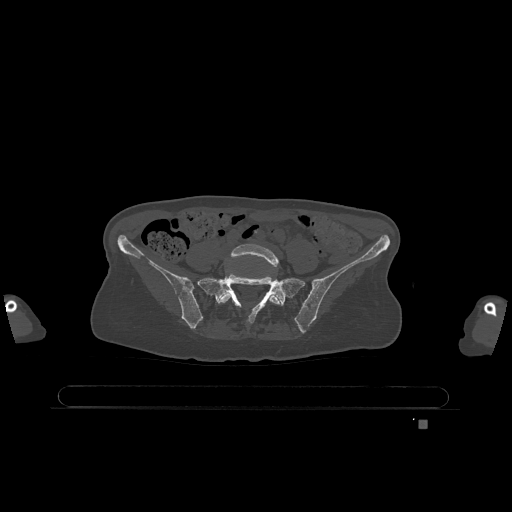
CT including the spine, one axial slice; bone window (W 1800 / L 400 HU); 512 × 512 image matrix, field of view 500 × 500 mm. Female patient, age 74 years. Case-level facts recorded for this patient, not image findings: primary cancer: lung; vertebrae with lytic lesions (as recorded): T1, T4, T5, T6, L4, L5.
Structures marked on this image (semi-automatic segmentation, software-assisted and operator-edited):
- L5 vertebra: box from (x=218, y=244) to (x=283, y=306) px